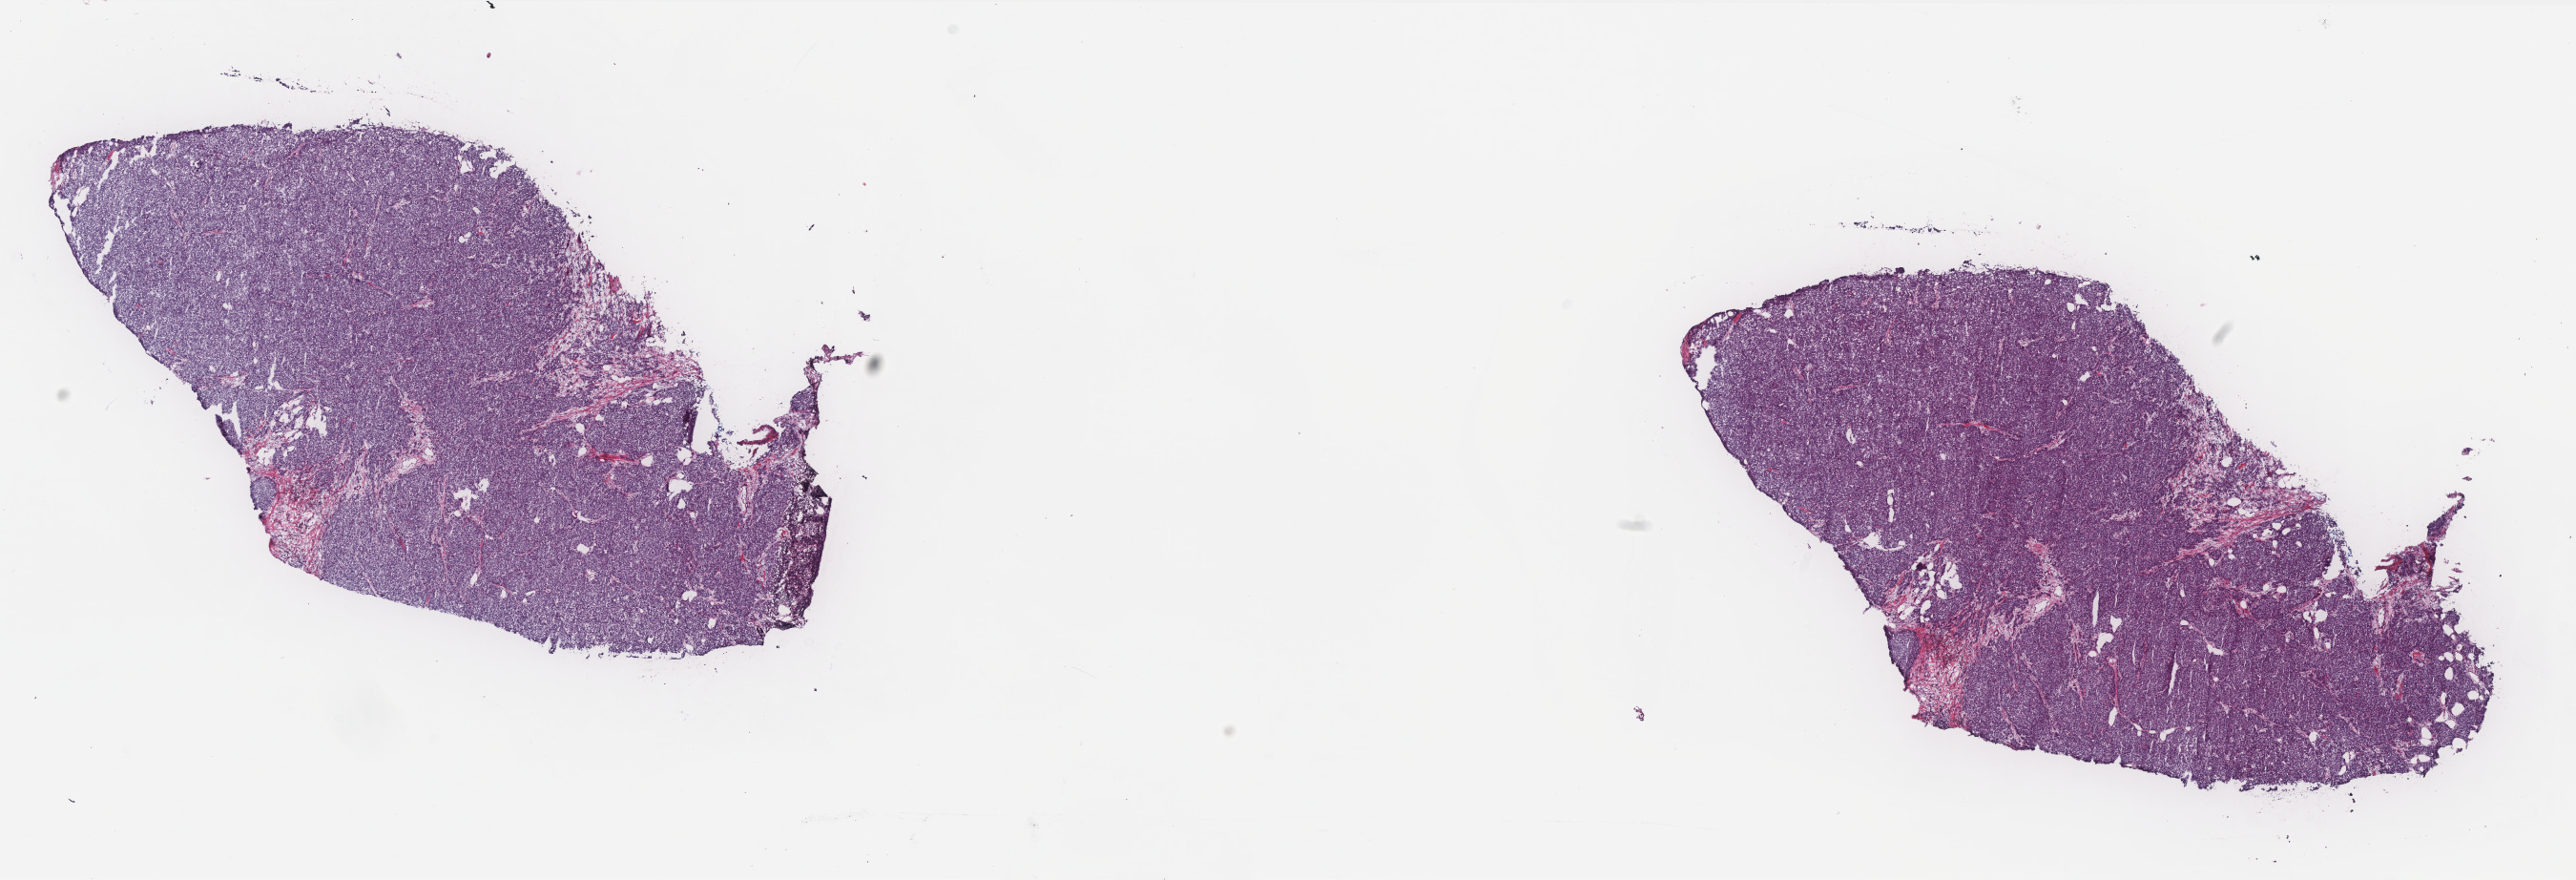
Digitized H&E tissue section (whole slide), low-resolution overview of the scanned area, about 21.6 x 7.4 mm (from a 40x scan); frozen section from the top of the tissue portion; primary tumour sample from the breast. Female patient; age at initial diagnosis 54 years. Composition of this section per pathologist review: tumour cells 95%, tumour nuclei 95%, normal cells 0%, stromal cells 5%, necrosis 0%. Inflammatory infiltration, as recorded: lymphocyte infiltration 1%, monocyte infiltration 1%, neutrophil infiltration 0%.
Laterality: right. Lymph nodes positive (case pathology): 2 of 22 examined. Diagnosis: Infiltrating duct carcinoma, NOS. AJCC pathologic stage: IIA (7th edition).